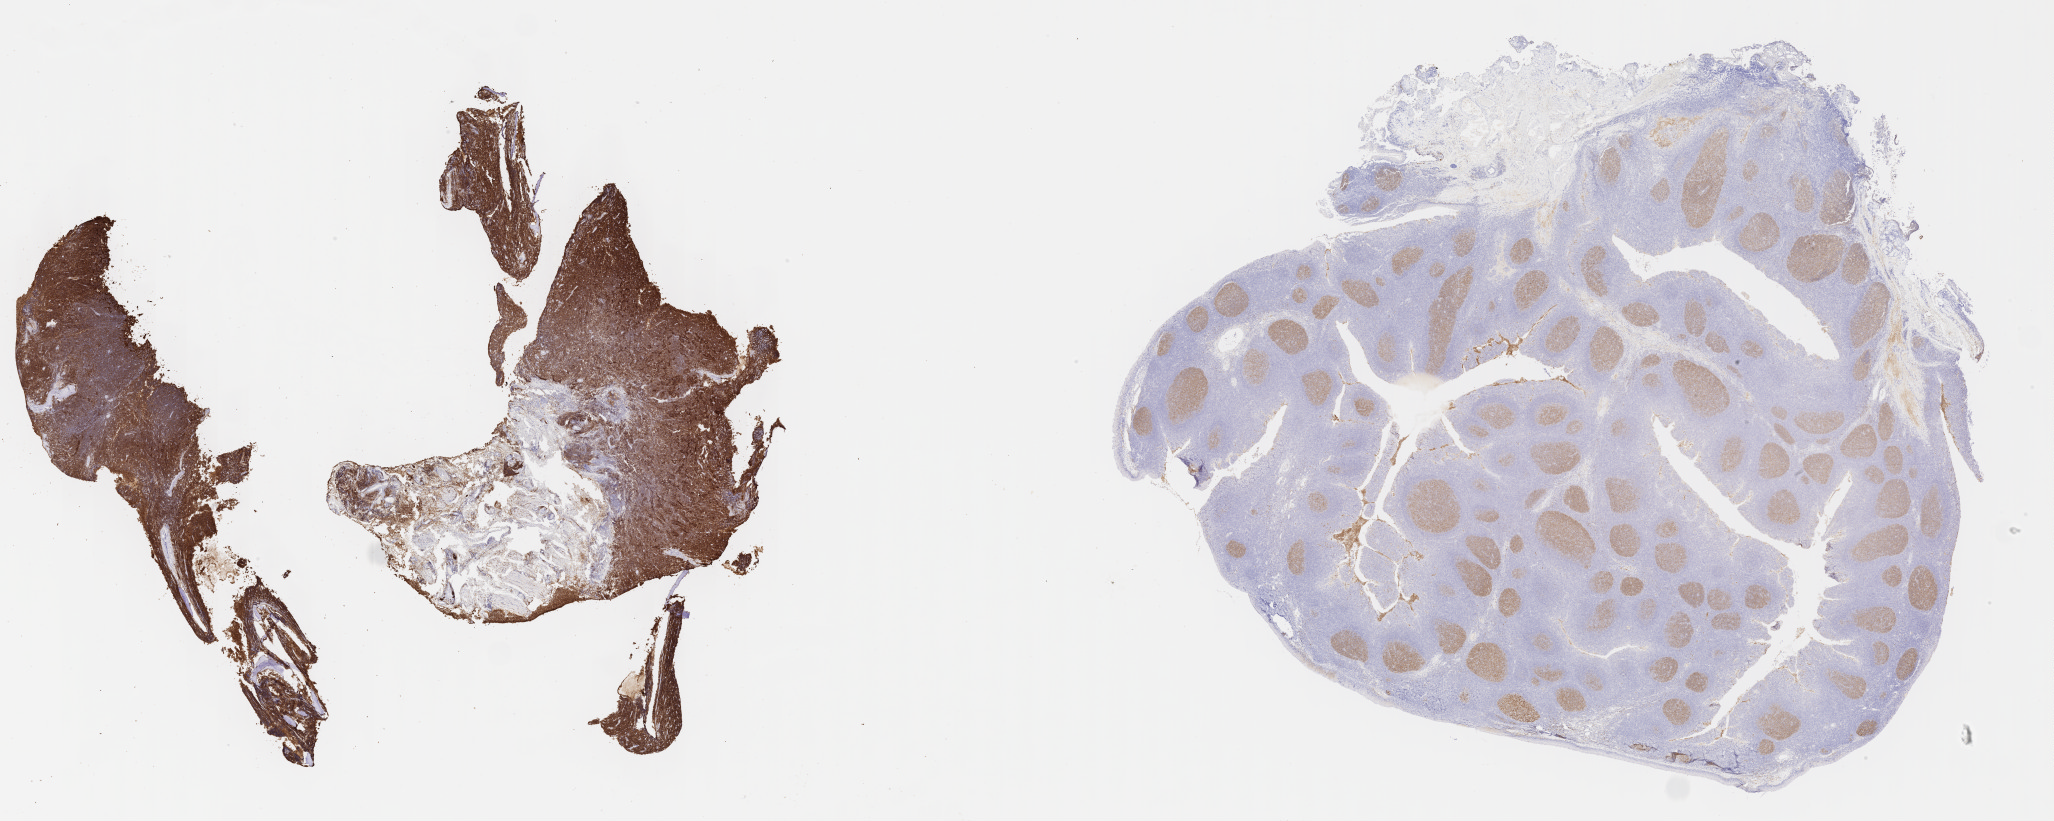
IHC for CD10, whole-slide image, whole scanned area (about 33.2 x 13.3 mm) shown as a low-resolution overview; specimen: tumor tissue; site: cranium. Patient: male, age at initial diagnosis 8 years.
Diagnosis: Burkitt lymphoma, NOS.